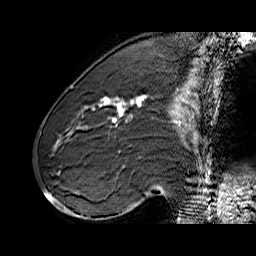
Breast MRI (dynamic contrast-enhanced), one sagittal slice. Position 24 of 60 along the scan axis. Dynamic contrast-enhanced series, time point 2 of 6 at this slice position (early post-contrast). 1.5 T. TE 6.4 ms, TR 32.9 ms. 256 × 256 image matrix, field of view 200 × 200 mm. Female patient. Case-level facts recorded for this patient, not image findings: setting: breast cancer imaged before/during neoadjuvant chemotherapy; receptor status: HER2-positive.
Annotated regions visible in this slice (semi-automatic segmentation, software-assisted and operator-edited):
- analysis volume of interest (the breast-tissue region the enhancement analysis was run in; not a lesion): bounding box (x1, y1, x2, y2) in pixels: (71, 80, 155, 146)
- tumour enhancement mask (voxels above the 100 % enhancement threshold inside the analysis volume of interest): (85, 96, 144, 119)